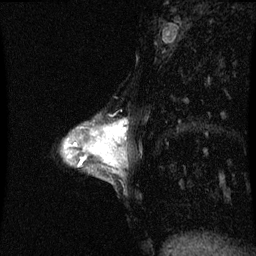
Breast MRI (dynamic contrast-enhanced), one sagittal slice; dynamic contrast-enhanced series, image 2 of 3 at this slice position (ordered by acquisition); 1.5 T; TE 4.2 ms, TR 8.9 ms; 256 × 256 image matrix, field of view 200 × 200 mm. Female patient, age 33 years. From the clinical record (not read from this slice): setting: breast cancer imaged before/during neoadjuvant chemotherapy; receptor status: HER2-positive.
Structures marked on this image (semi-automatic segmentation, software-assisted and operator-edited):
- analysis volume of interest (the breast-tissue region the enhancement analysis was run in; not a lesion): bounding box [x1, y1, x2, y2] px = [95, 124, 127, 153]
- tumour enhancement mask (voxels above the 70 % enhancement threshold inside the analysis volume of interest): [113, 126, 122, 141]